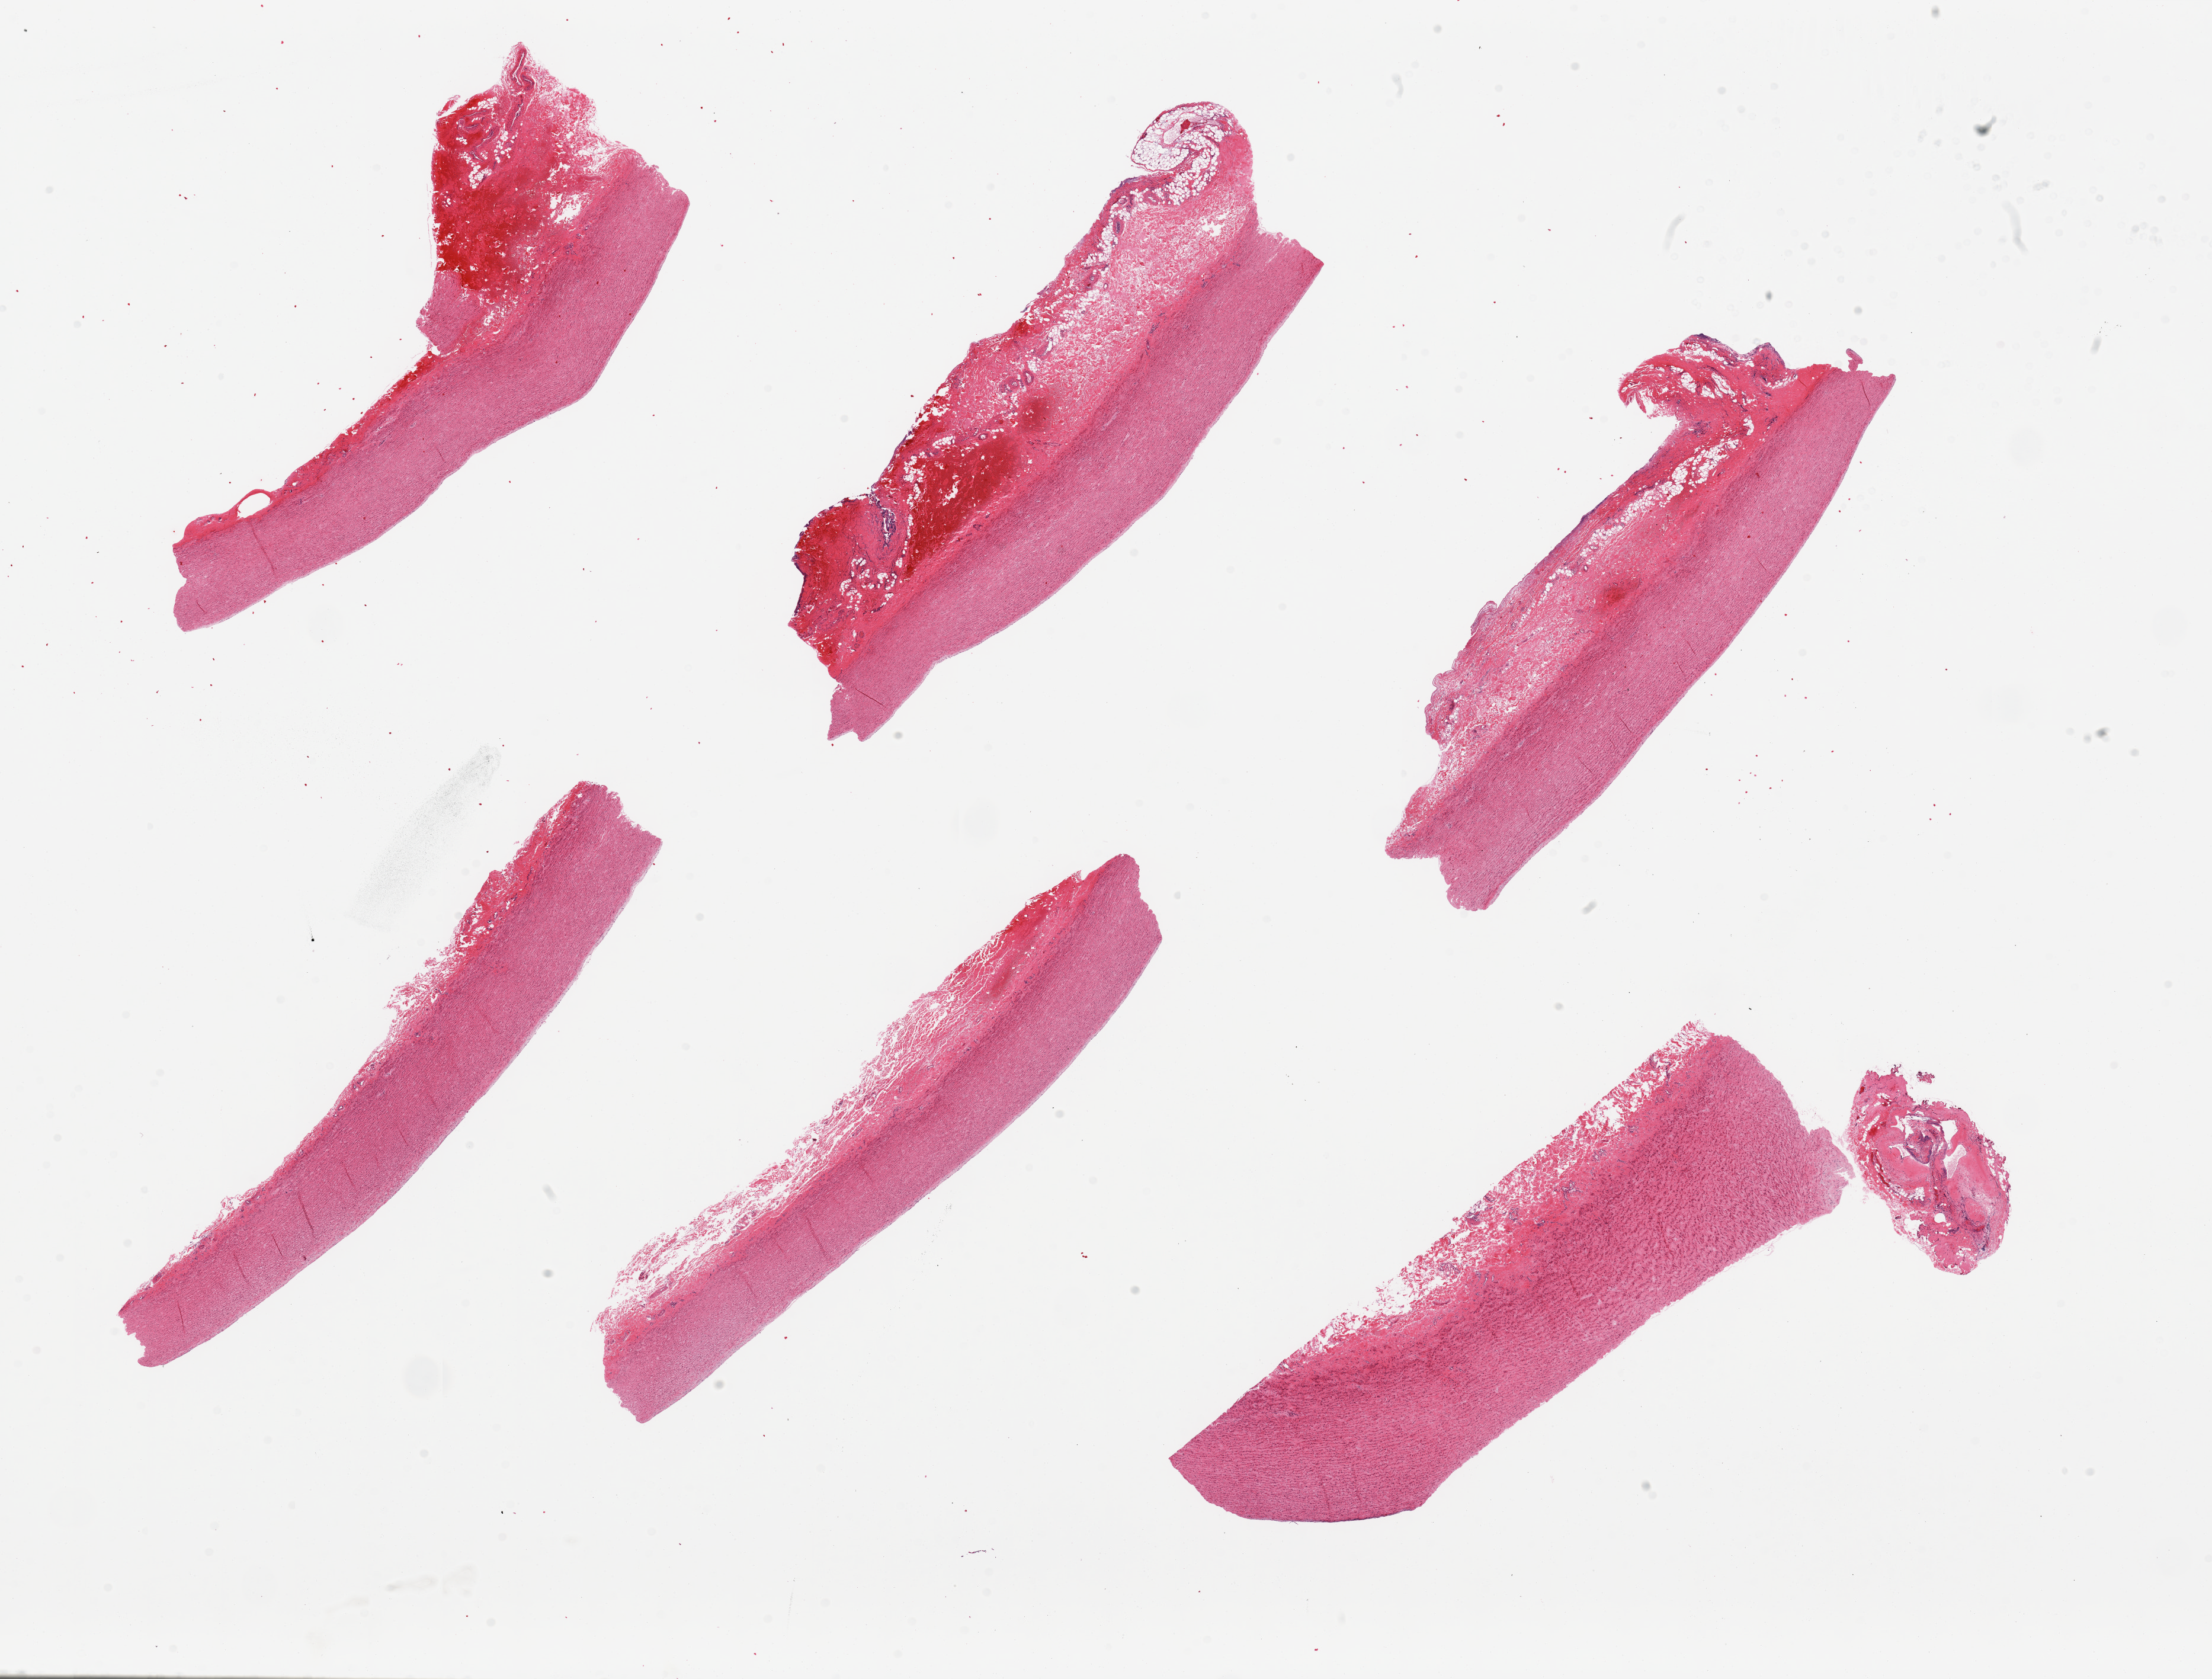
Digitized H&E-stained section, a low-resolution overview of the entire scanned area, about 29.5 x 22.4 mm (slide scanned at 20x), PAXgene-fixed, paraffin-embedded tissue, target tissue: aorta, donor tissue sample. Donor sex: female.
Pathologist's review note for this sample: 6 pieces, hemorrhage in adventitia.